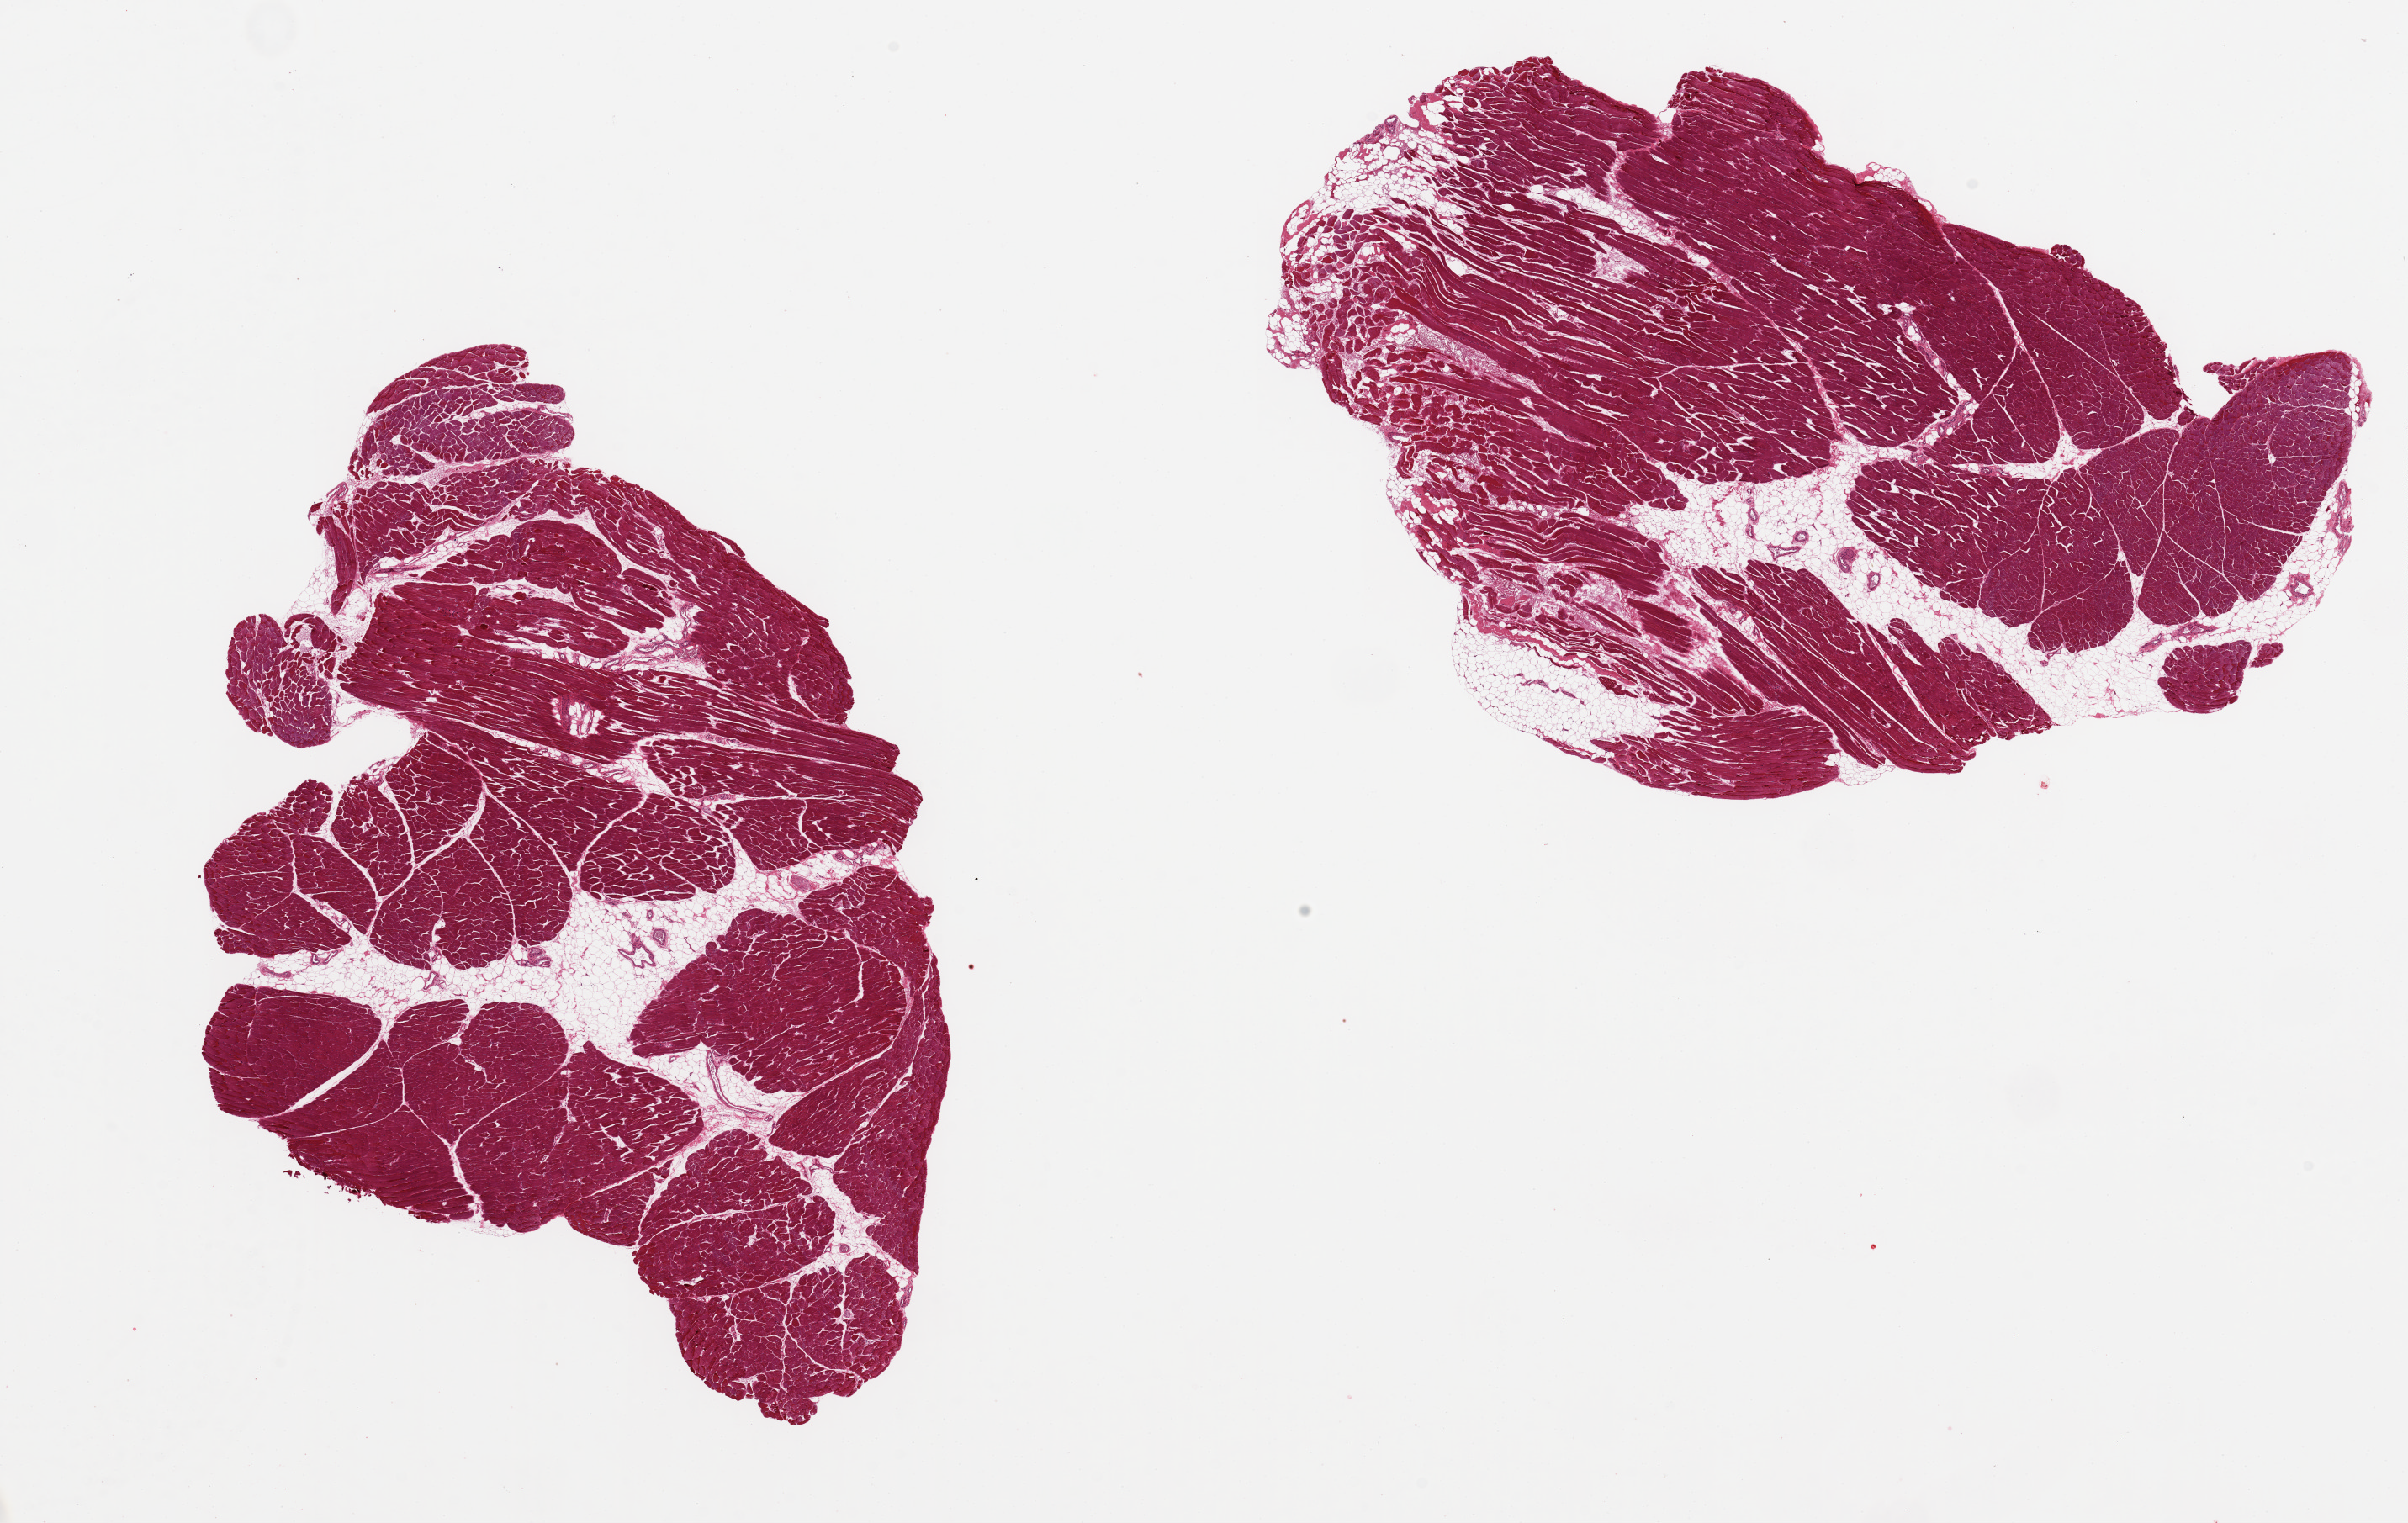
Haematoxylin and eosin whole-slide image — a low-resolution overview of the entire scanned area, about 22.6 x 14.3 mm (slide scanned at 20x); PAXgene-fixed paraffin-embedded (PFPE) section; sampled site (target tissue): skeletal muscle; tissue donor sample. Donor sex: male.
- reviewer comment on this tissue sample: 2 aliquots, ~9x7mm. Moderte interstitial fat